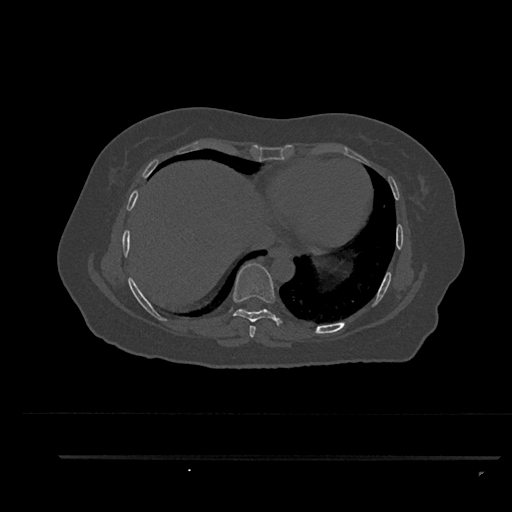
CT including the spine, one axial slice. Slice 458 of 797 in the series (ordered by position). Bone window (W 1800 / L 400 HU). 0.5 mm slice thickness. 512 × 512 image matrix, field of view 408 × 408 mm. Female patient, age 44 years. Case-level facts recorded for this patient, not image findings: primary cancer: renal; vertebrae with lytic lesions (as recorded): L1.
Outlined on this slice (semi-automatically segmented with operator editing):
- T7 vertebra: box from (x=249, y=326) to (x=256, y=338) px
- T8 vertebra: (x=233, y=262)–(x=284, y=326)